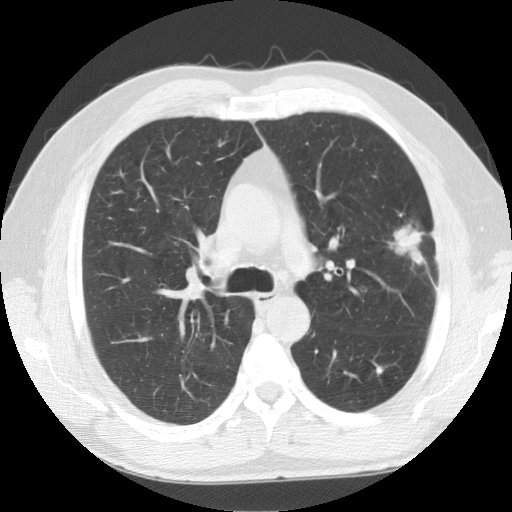
Low-dose screening chest CT, axial slice, baseline annual screen, lung window (W 1500 / L -600 HU), 2.5 mm slice thickness, standard (soft-tissue) reconstruction kernel (STANDARD), 512 × 512 image matrix, field of view 360 × 360 mm. Male, age 59 years at enrolment. Former smoker at enrolment.
- Expert-annotated lung lesion, box from (x=372, y=204) to (x=453, y=282) px.
- Reader record for this screening exam (exam-level; its link to the box is not recorded): non-calcified nodule or mass ≥4 mm, left upper lobe, 23 × 23 mm, spiculated (stellate) margins, soft tissue attenuation.
- Official screen result: positive, change unspecified: nodule(s) >= 4 mm or enlarging nodule(s), mass(es), or other non-specific abnormalities suspicious for lung cancer.
- Later outcome: lung cancer diagnosed 28 days after this screen — squamous cell carcinoma, NOS, left upper lobe, moderately differentiated (G2), stage IA (AJCC 6th edition), 27 mm at pathology.